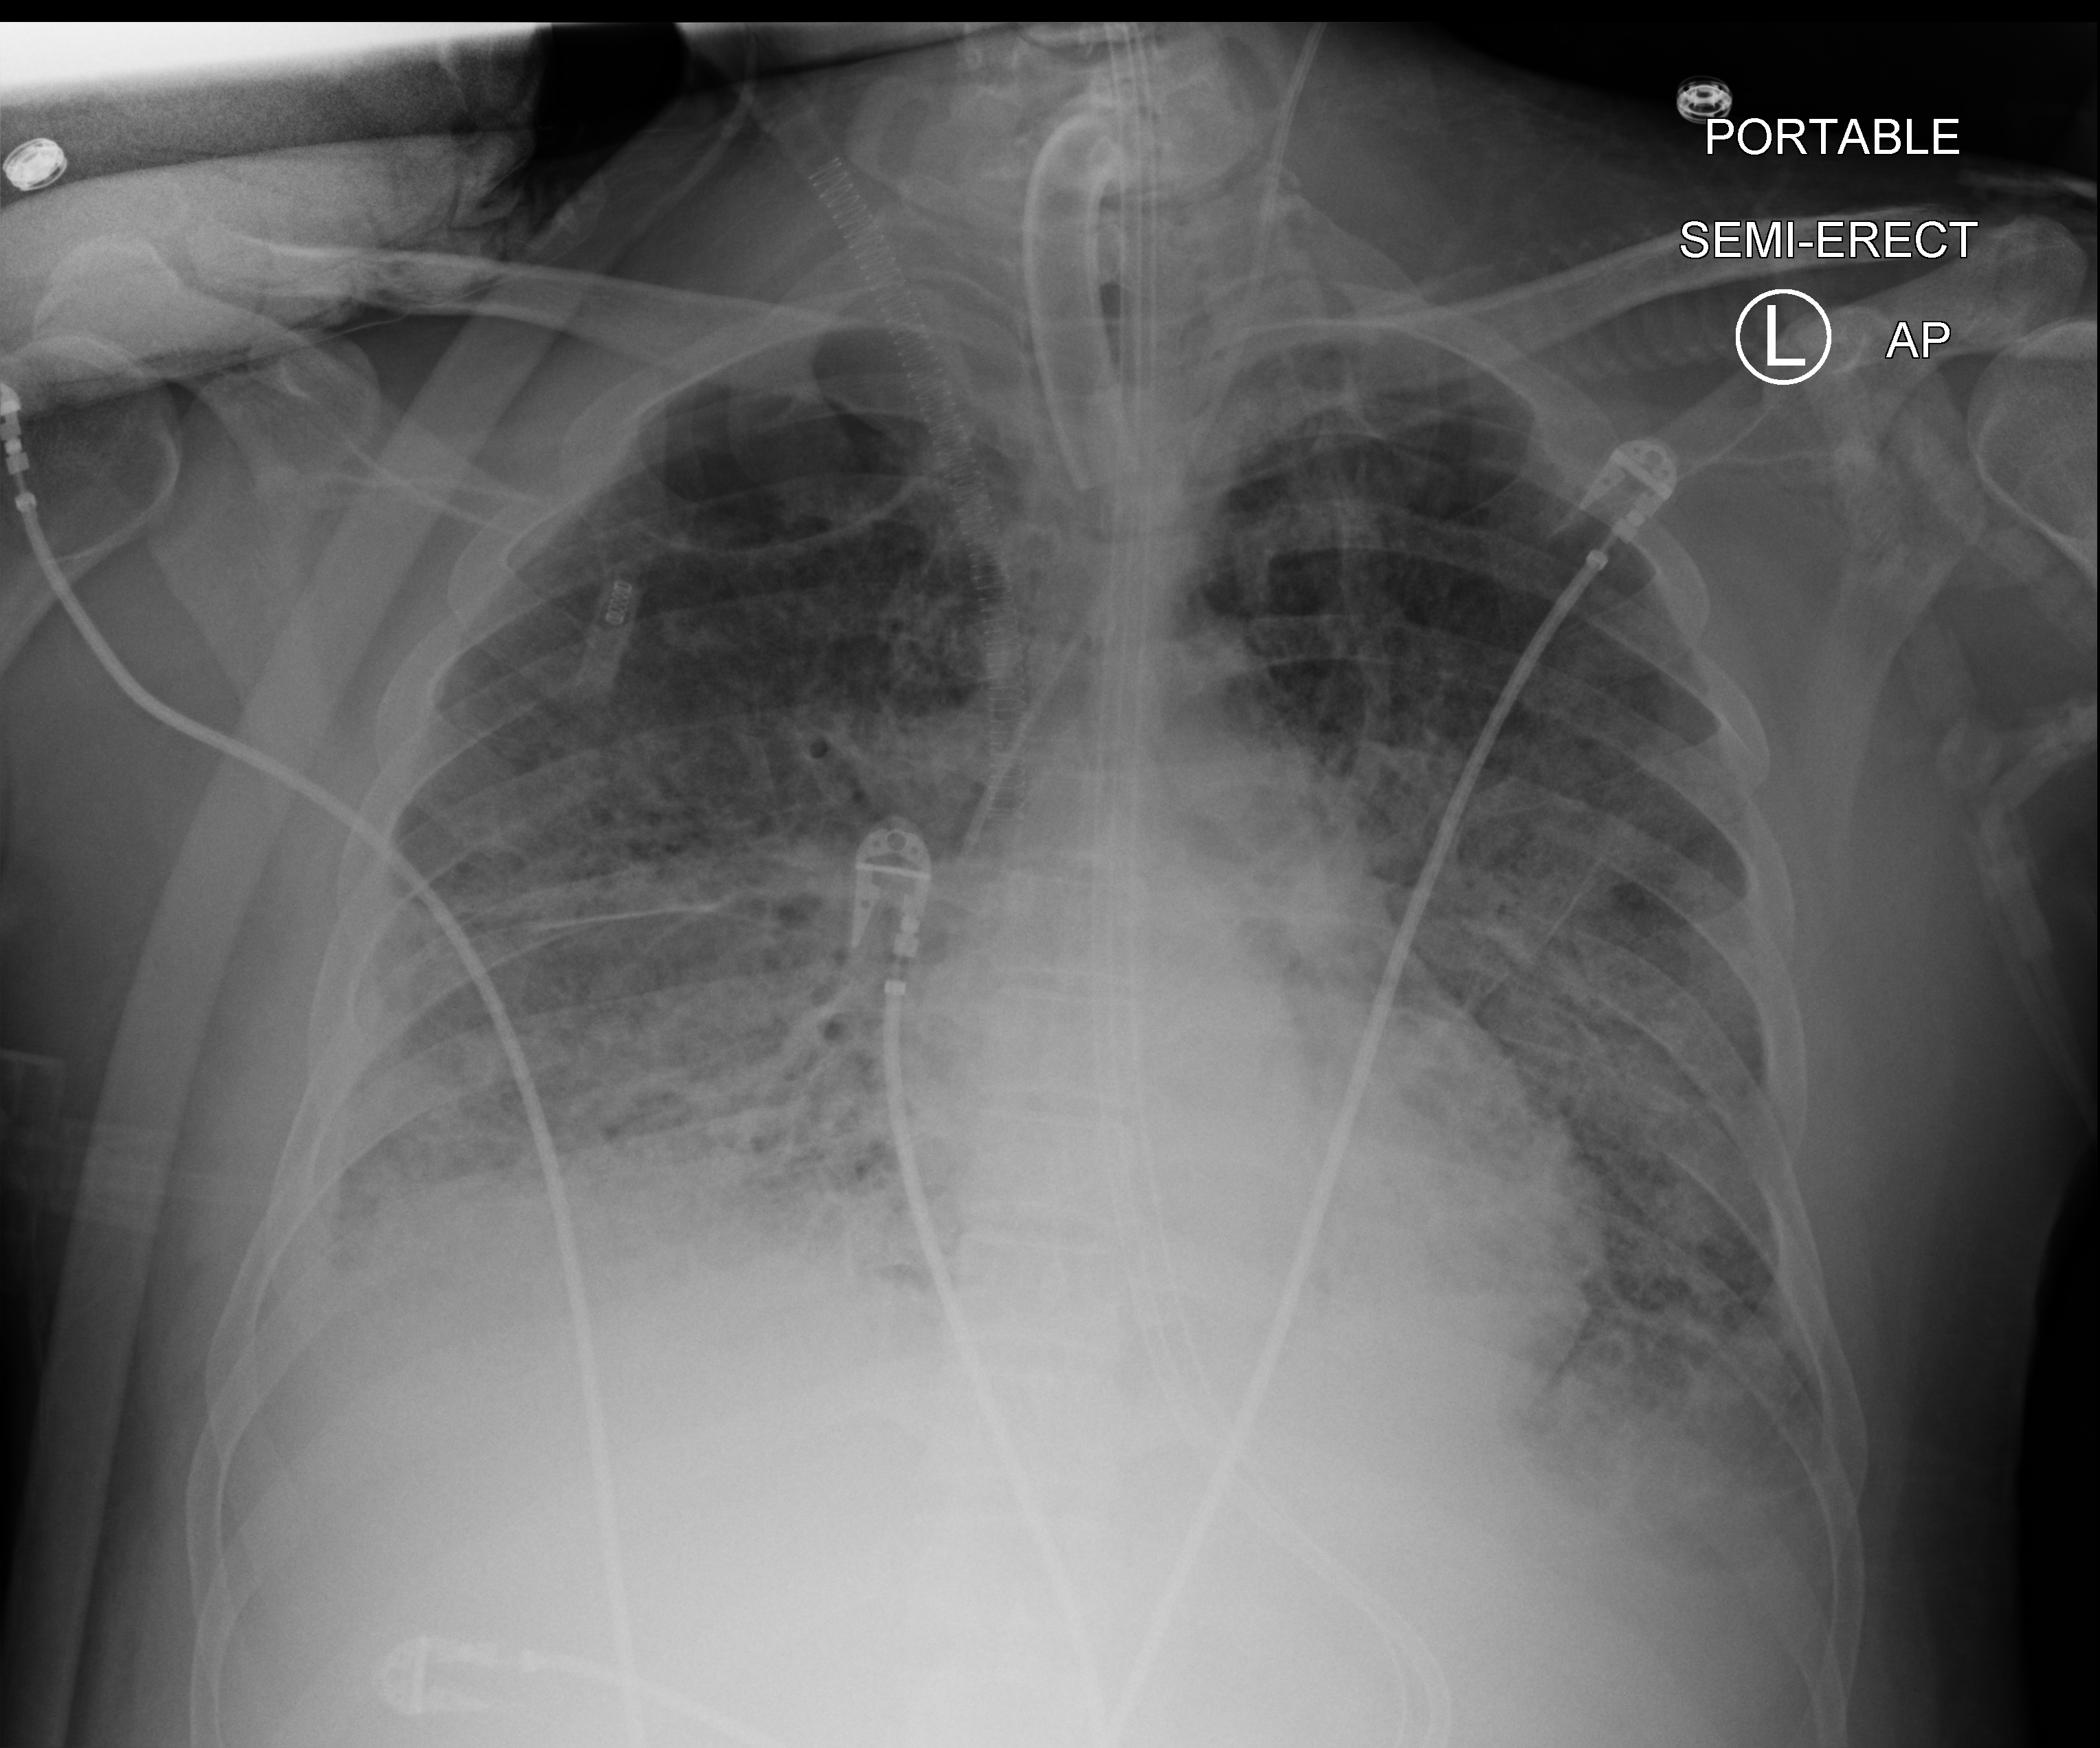
Portable chest radiograph, anteroposterior (AP) projection. Adult patient hospitalised with COVID-19, age 18–59 years.
Hospital-stay facts (about this admission, not read from this image; timing relative to this image not recorded): chronic kidney disease (admission record): no; mechanically ventilated during this hospital stay: yes; COPD (admission record): no.